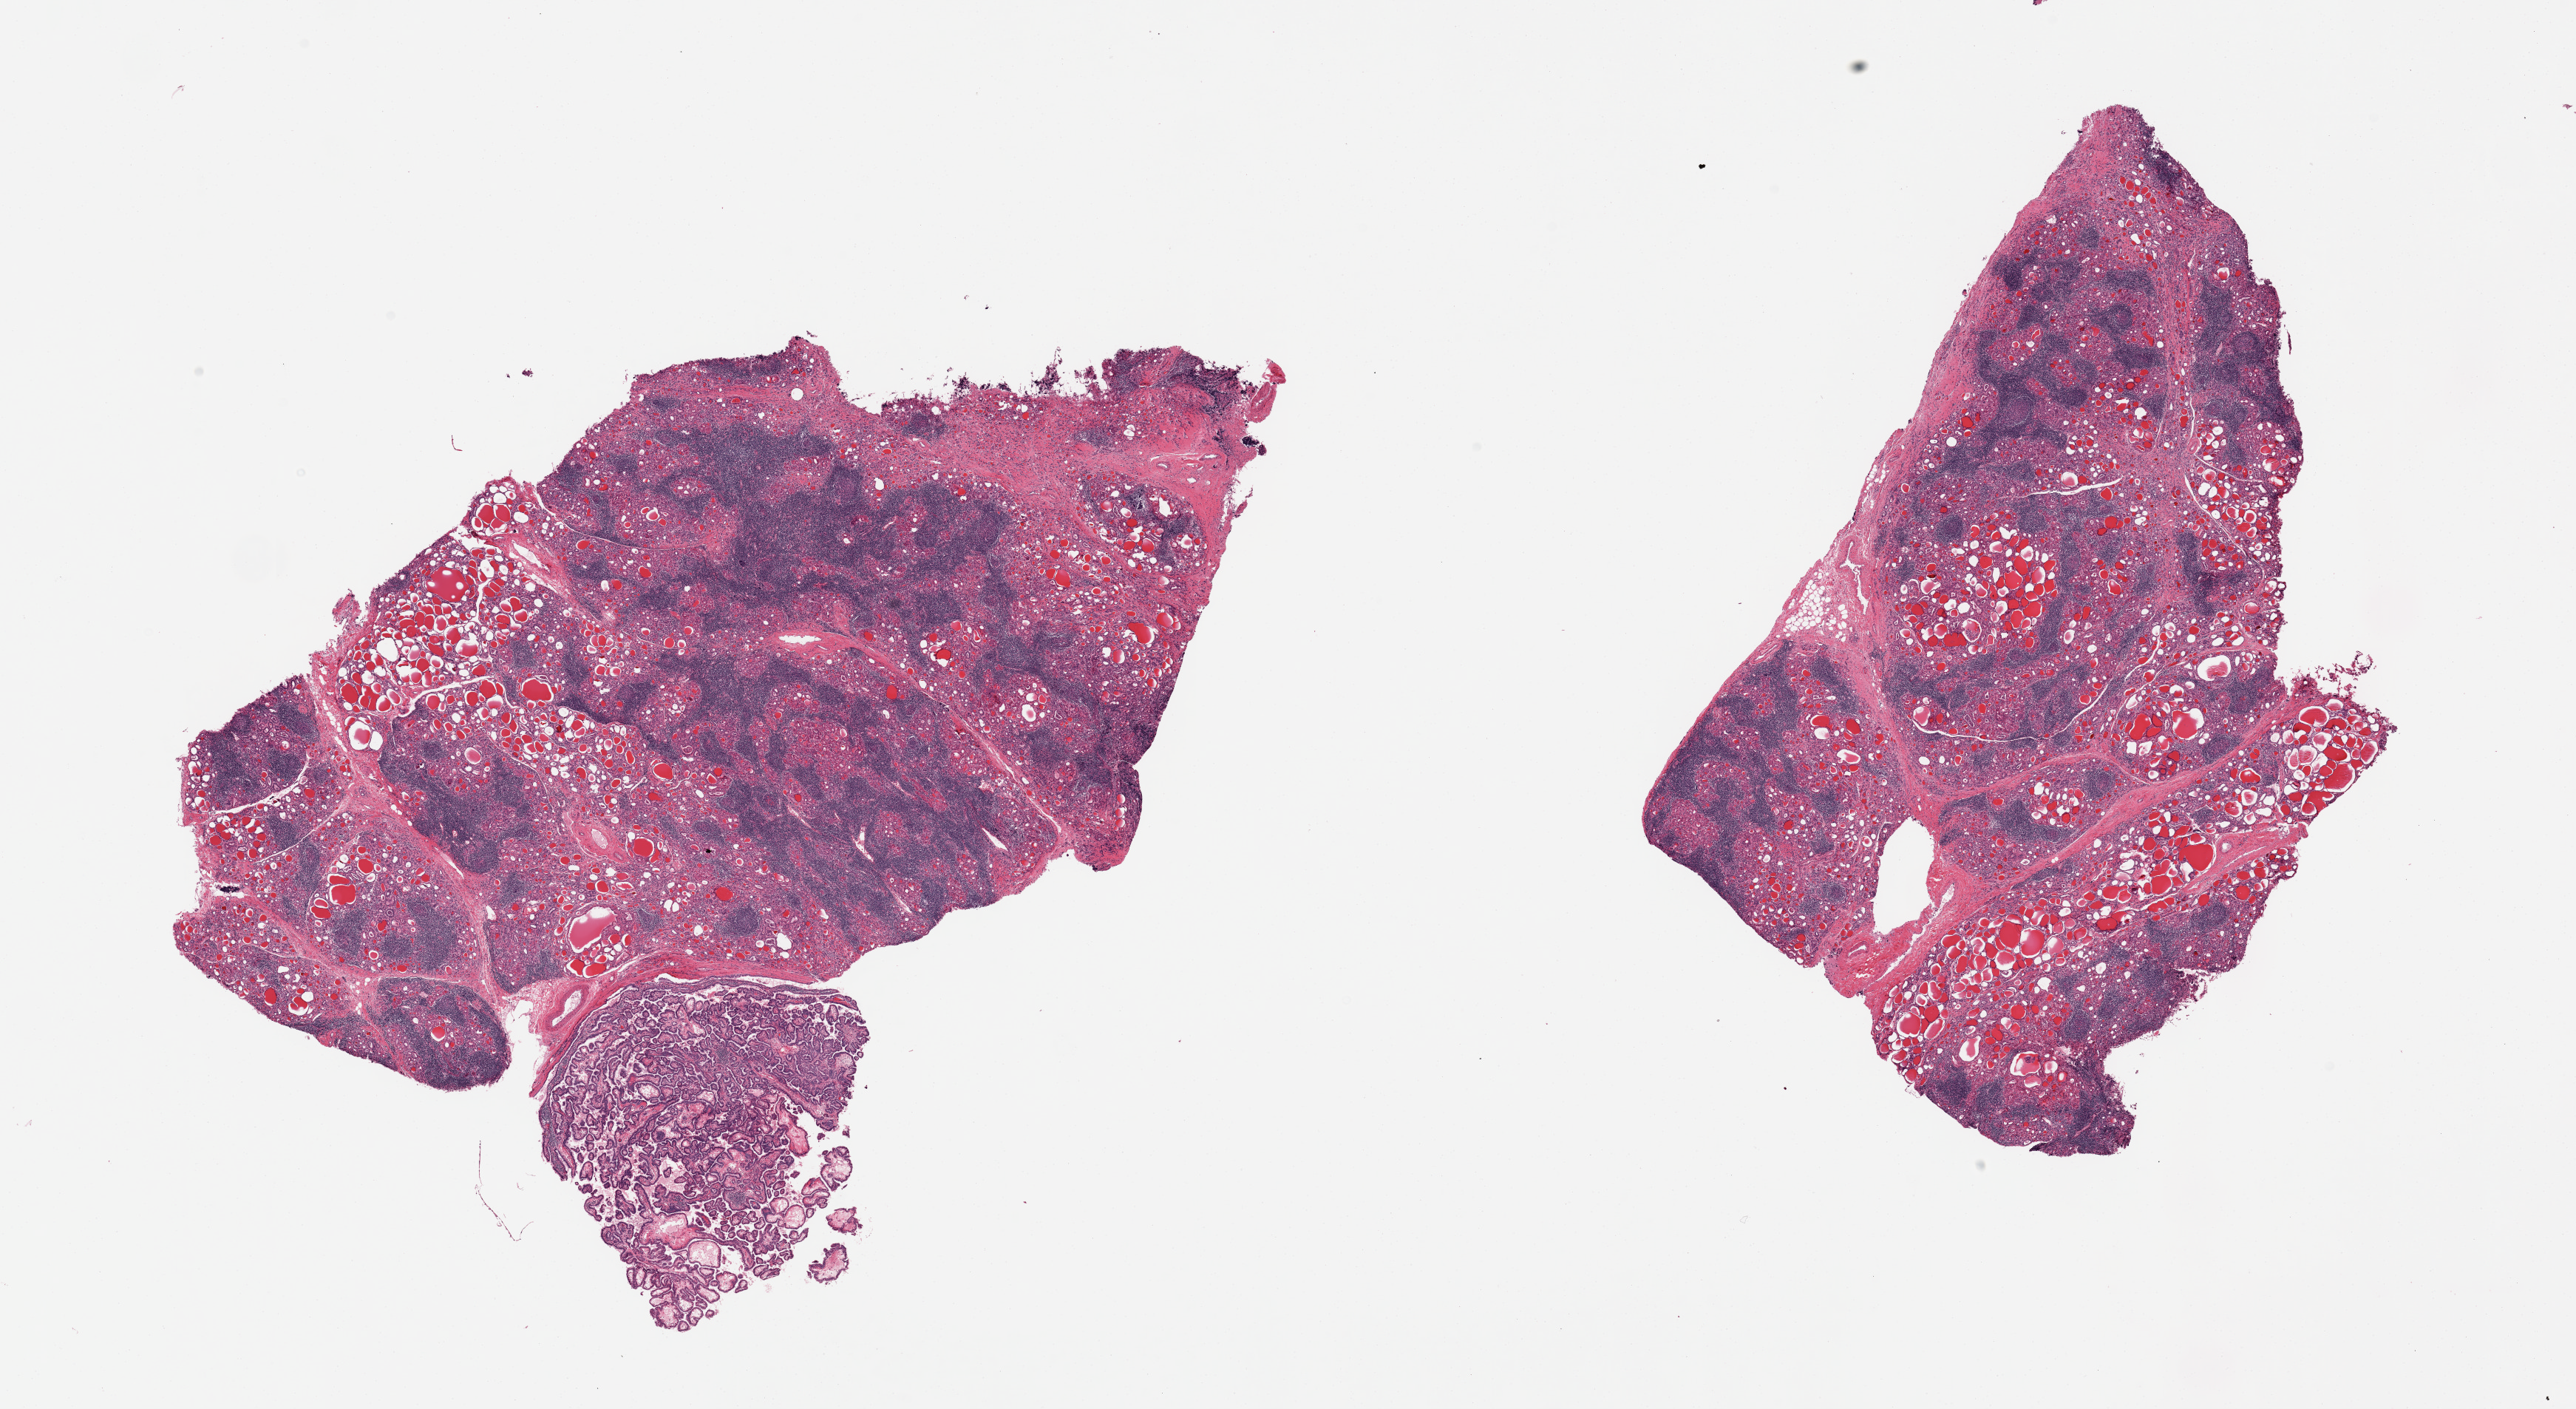
Digitized haematoxylin and eosin-stained section, shown as a low-resolution overview of the whole scanned area (about 27.6 x 15.1 mm, from a 20x scan), PAXgene-fixed, paraffin-embedded tissue, target tissue: thyroid, donor tissue sample. Donor: female.
Pathologist's review note for this sample: 2 pieces. Papillary carcinoma [3.3 mm]. Hashimoto thyroiditis, moderate degree.